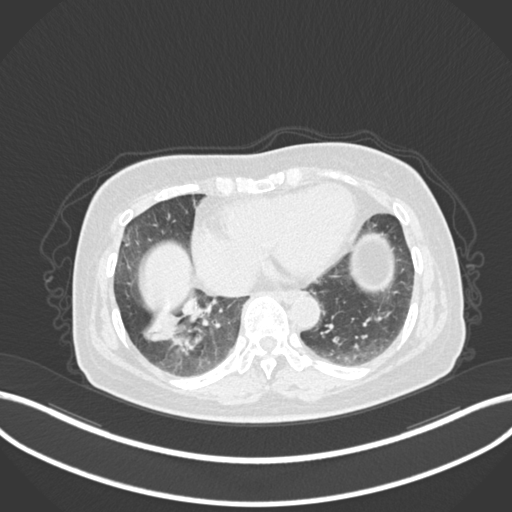
Chest CT, one axial slice; slice 36 of 222 in the series (ordered by position); lung window (W 1500 / L -600 HU); 1 mm slice thickness; 512 × 512 image matrix, field of view 400 × 400 mm. Patient: female, 67 years. Case-level facts recorded for this patient, not image findings: clinical TNM (as recorded): T1c N1 M0; histopathological grade: G2-3.
Outlined on this slice (rectangle marked by the reading radiologist):
- lung tumour (recorded histology: adenocarcinoma): bounding box [x1, y1, x2, y2] px = [137, 300, 227, 357]